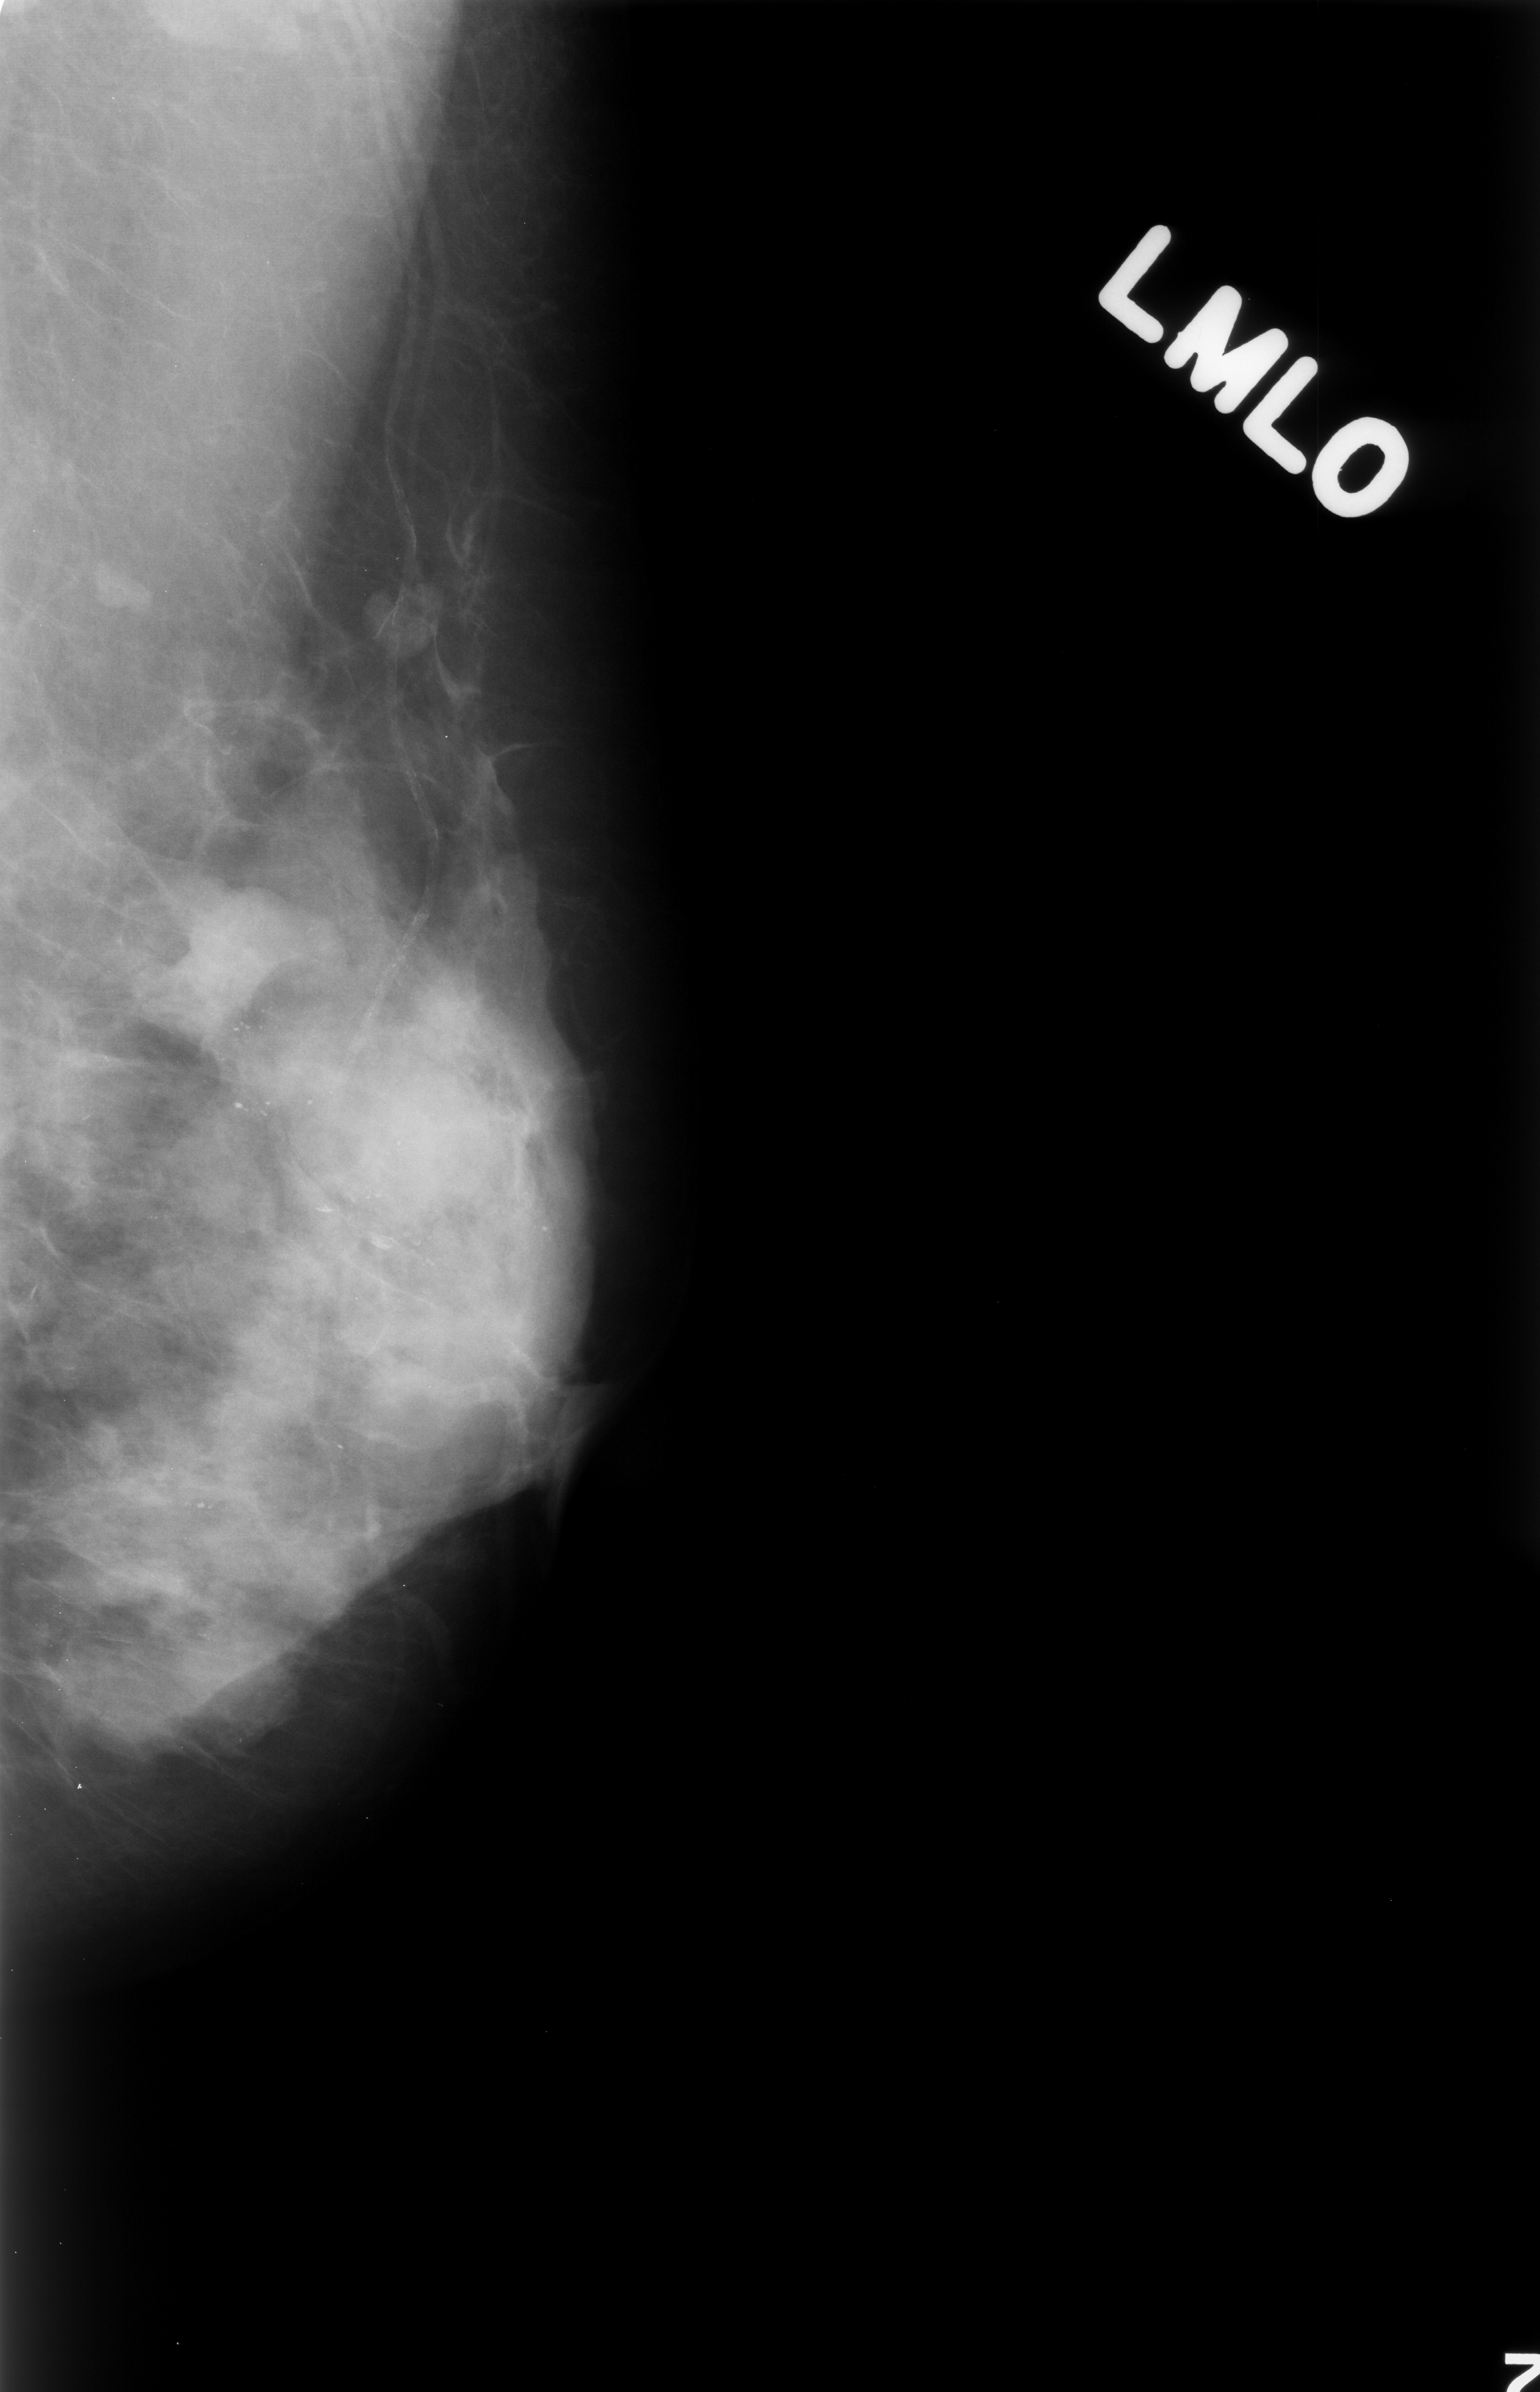
Digitized screen-film mammogram; left breast; mediolateral oblique (MLO) view.
- Marked findings (only marked abnormalities are described; nothing is implied about the rest of the image): Finding 1 of 2: mass, shape lobulated, margins obscured; BI-RADS assessment category 3; pathology (as recorded): benign.
- Finding 2 of 2: mass, shape oval, margins circumscribed; BI-RADS assessment category 3; subtlety rating 3 on a 1 (subtle) to 5 (obvious) scale; pathology (as recorded): benign.